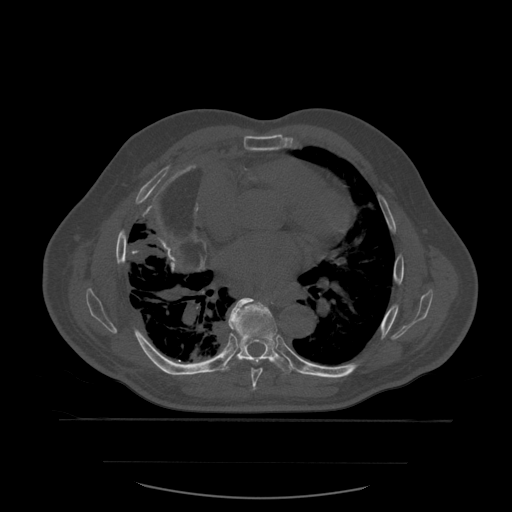
CT including the spine, one axial slice; position 371 of 590 along the scan axis; bone window (W 1800 / L 400 HU); 512 × 512 image matrix, field of view 479 × 479 mm. Patient age 71 years. Case-level facts recorded for this patient, not image findings: primary cancer: lung; vertebrae with lytic lesions (as recorded): T1, T2, L5, S1.
Annotated regions visible in this slice (semi-automatic segmentation, software-assisted and operator-edited):
- T7 vertebra: bounding box (x1, y1, x2, y2) in pixels: (232, 298, 263, 391)
- T8 vertebra: (223, 299, 294, 375)